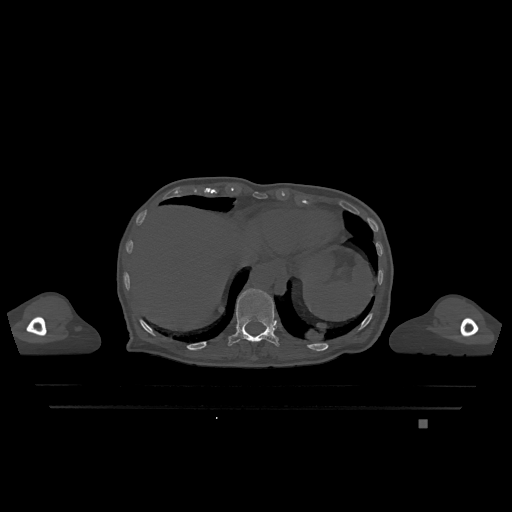
CT including the spine, one axial slice. Position 592 of 1317 along the scan axis. Bone window (W 1800 / L 400 HU). 0.5 mm slice thickness. 512 × 512 image matrix, field of view 500 × 500 mm. Patient: female, 74 years. From the clinical record (not read from this slice): primary cancer: lung; vertebrae with lytic lesions (as recorded): T1, T4, T5, T6, L4, L5.
Outlined on this slice (semi-automatically segmented with operator editing):
- T11 vertebra: box from (x=228, y=289) to (x=280, y=347) px